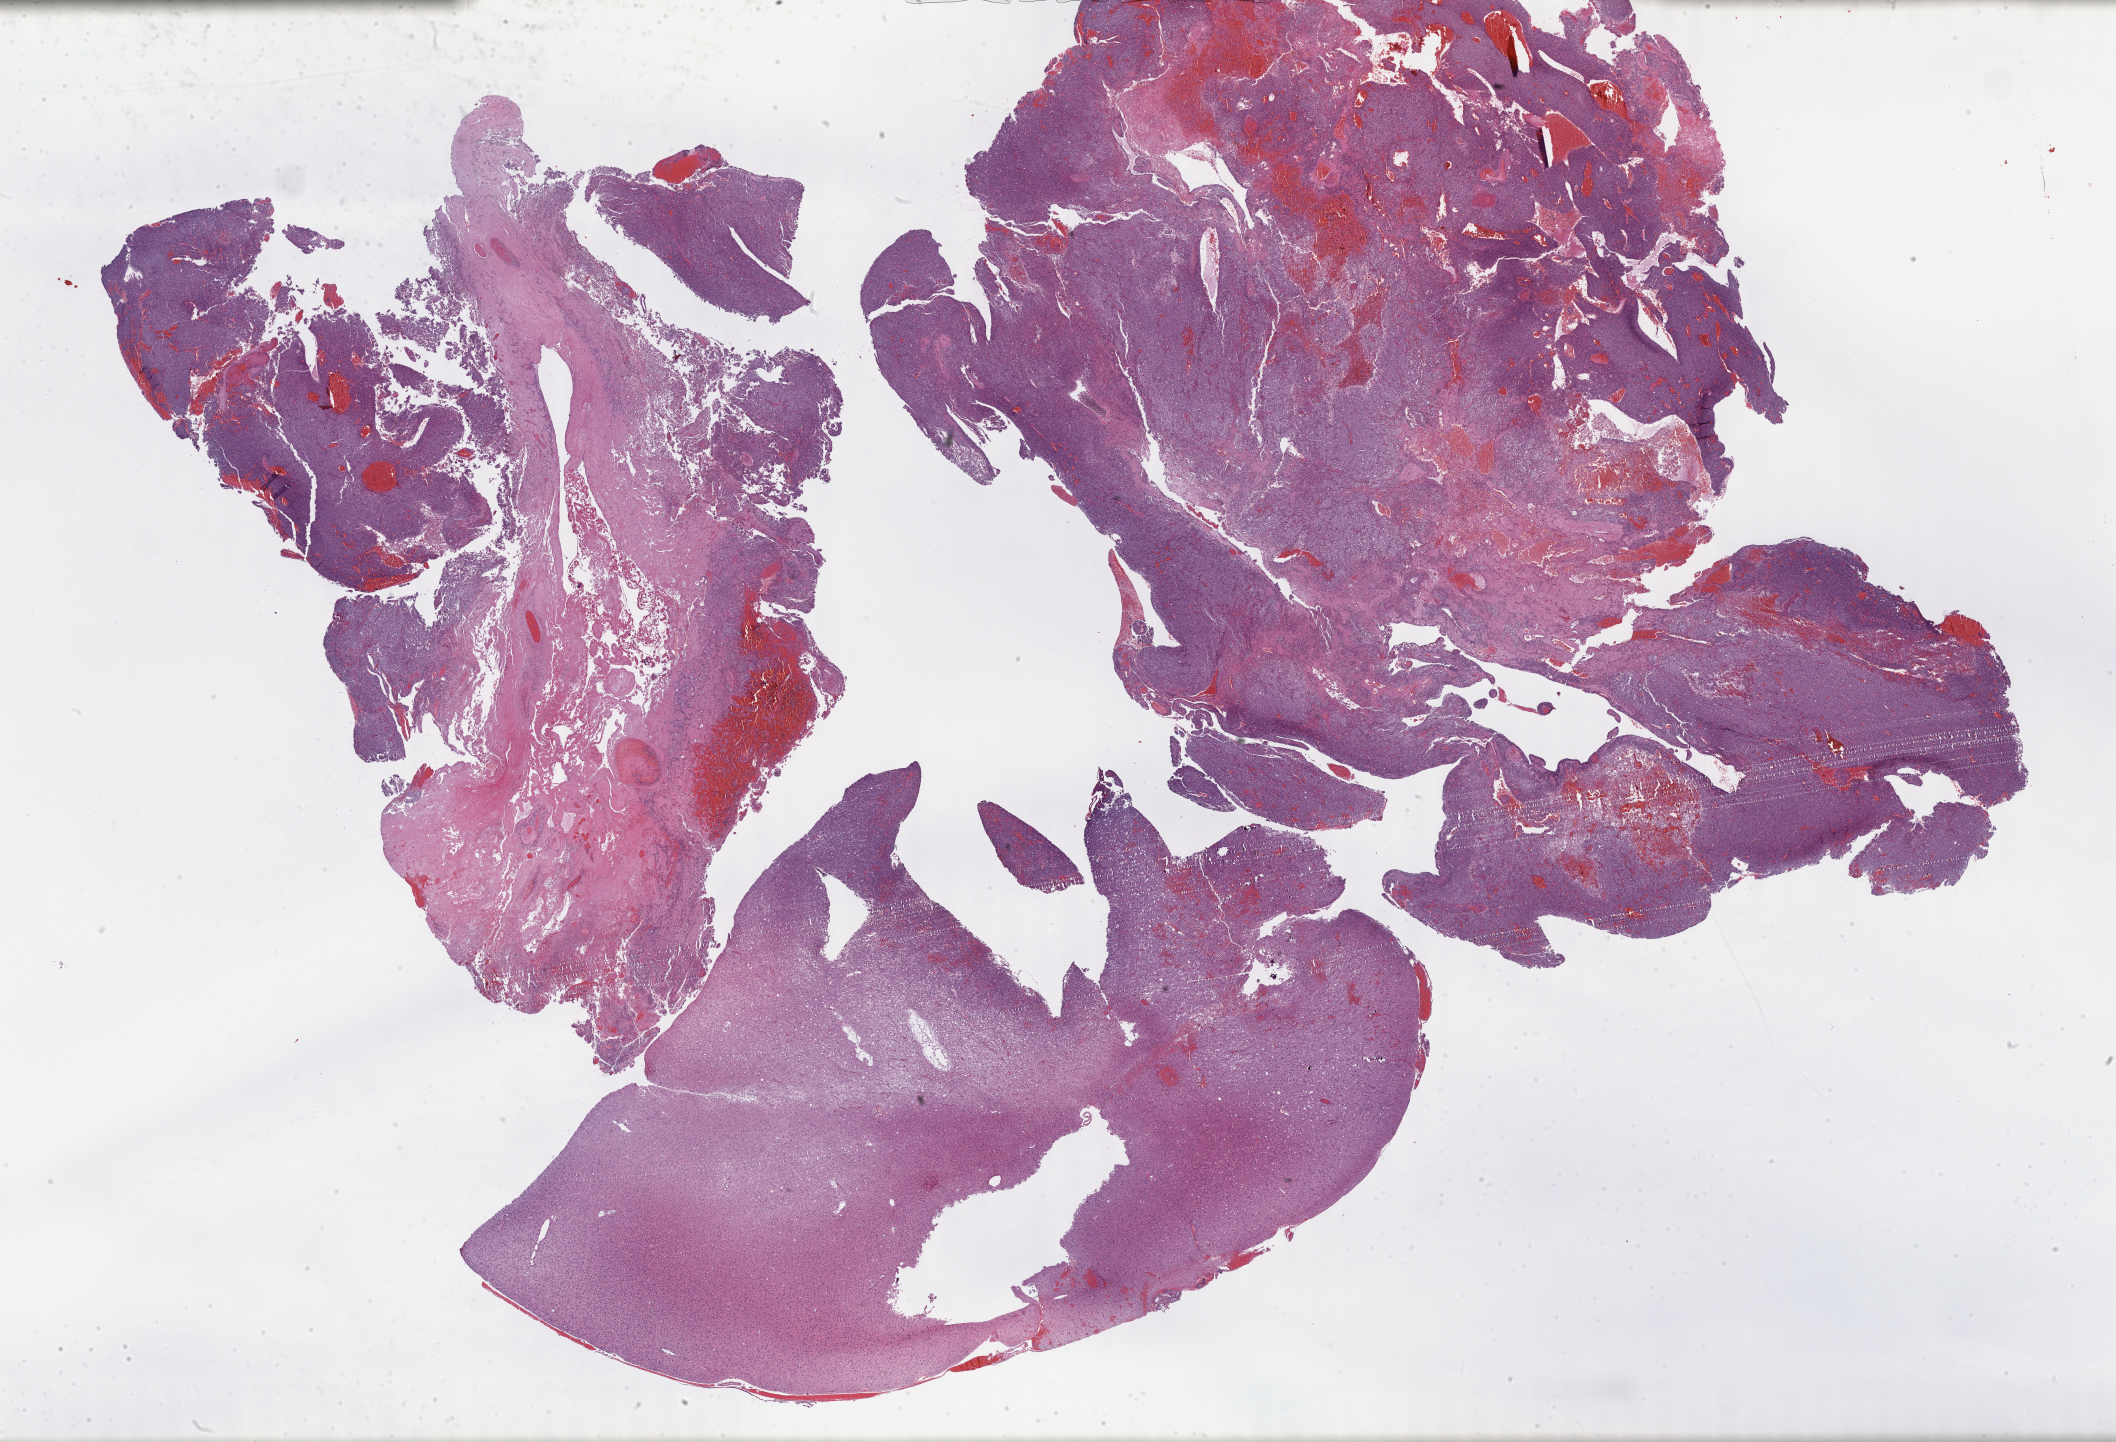
Whole-slide histology image, H&E-stained, whole scanned area (about 34.2 x 23.3 mm, slide scanned at 40x) shown as a low-resolution overview, FFPE section, sample: primary tumour, brain. Patient: male, age at initial diagnosis 33 years. Histologic grade: G3 (poorly differentiated).
Pathologic diagnosis: Oligodendroglioma, anaplastic (cerebrum).